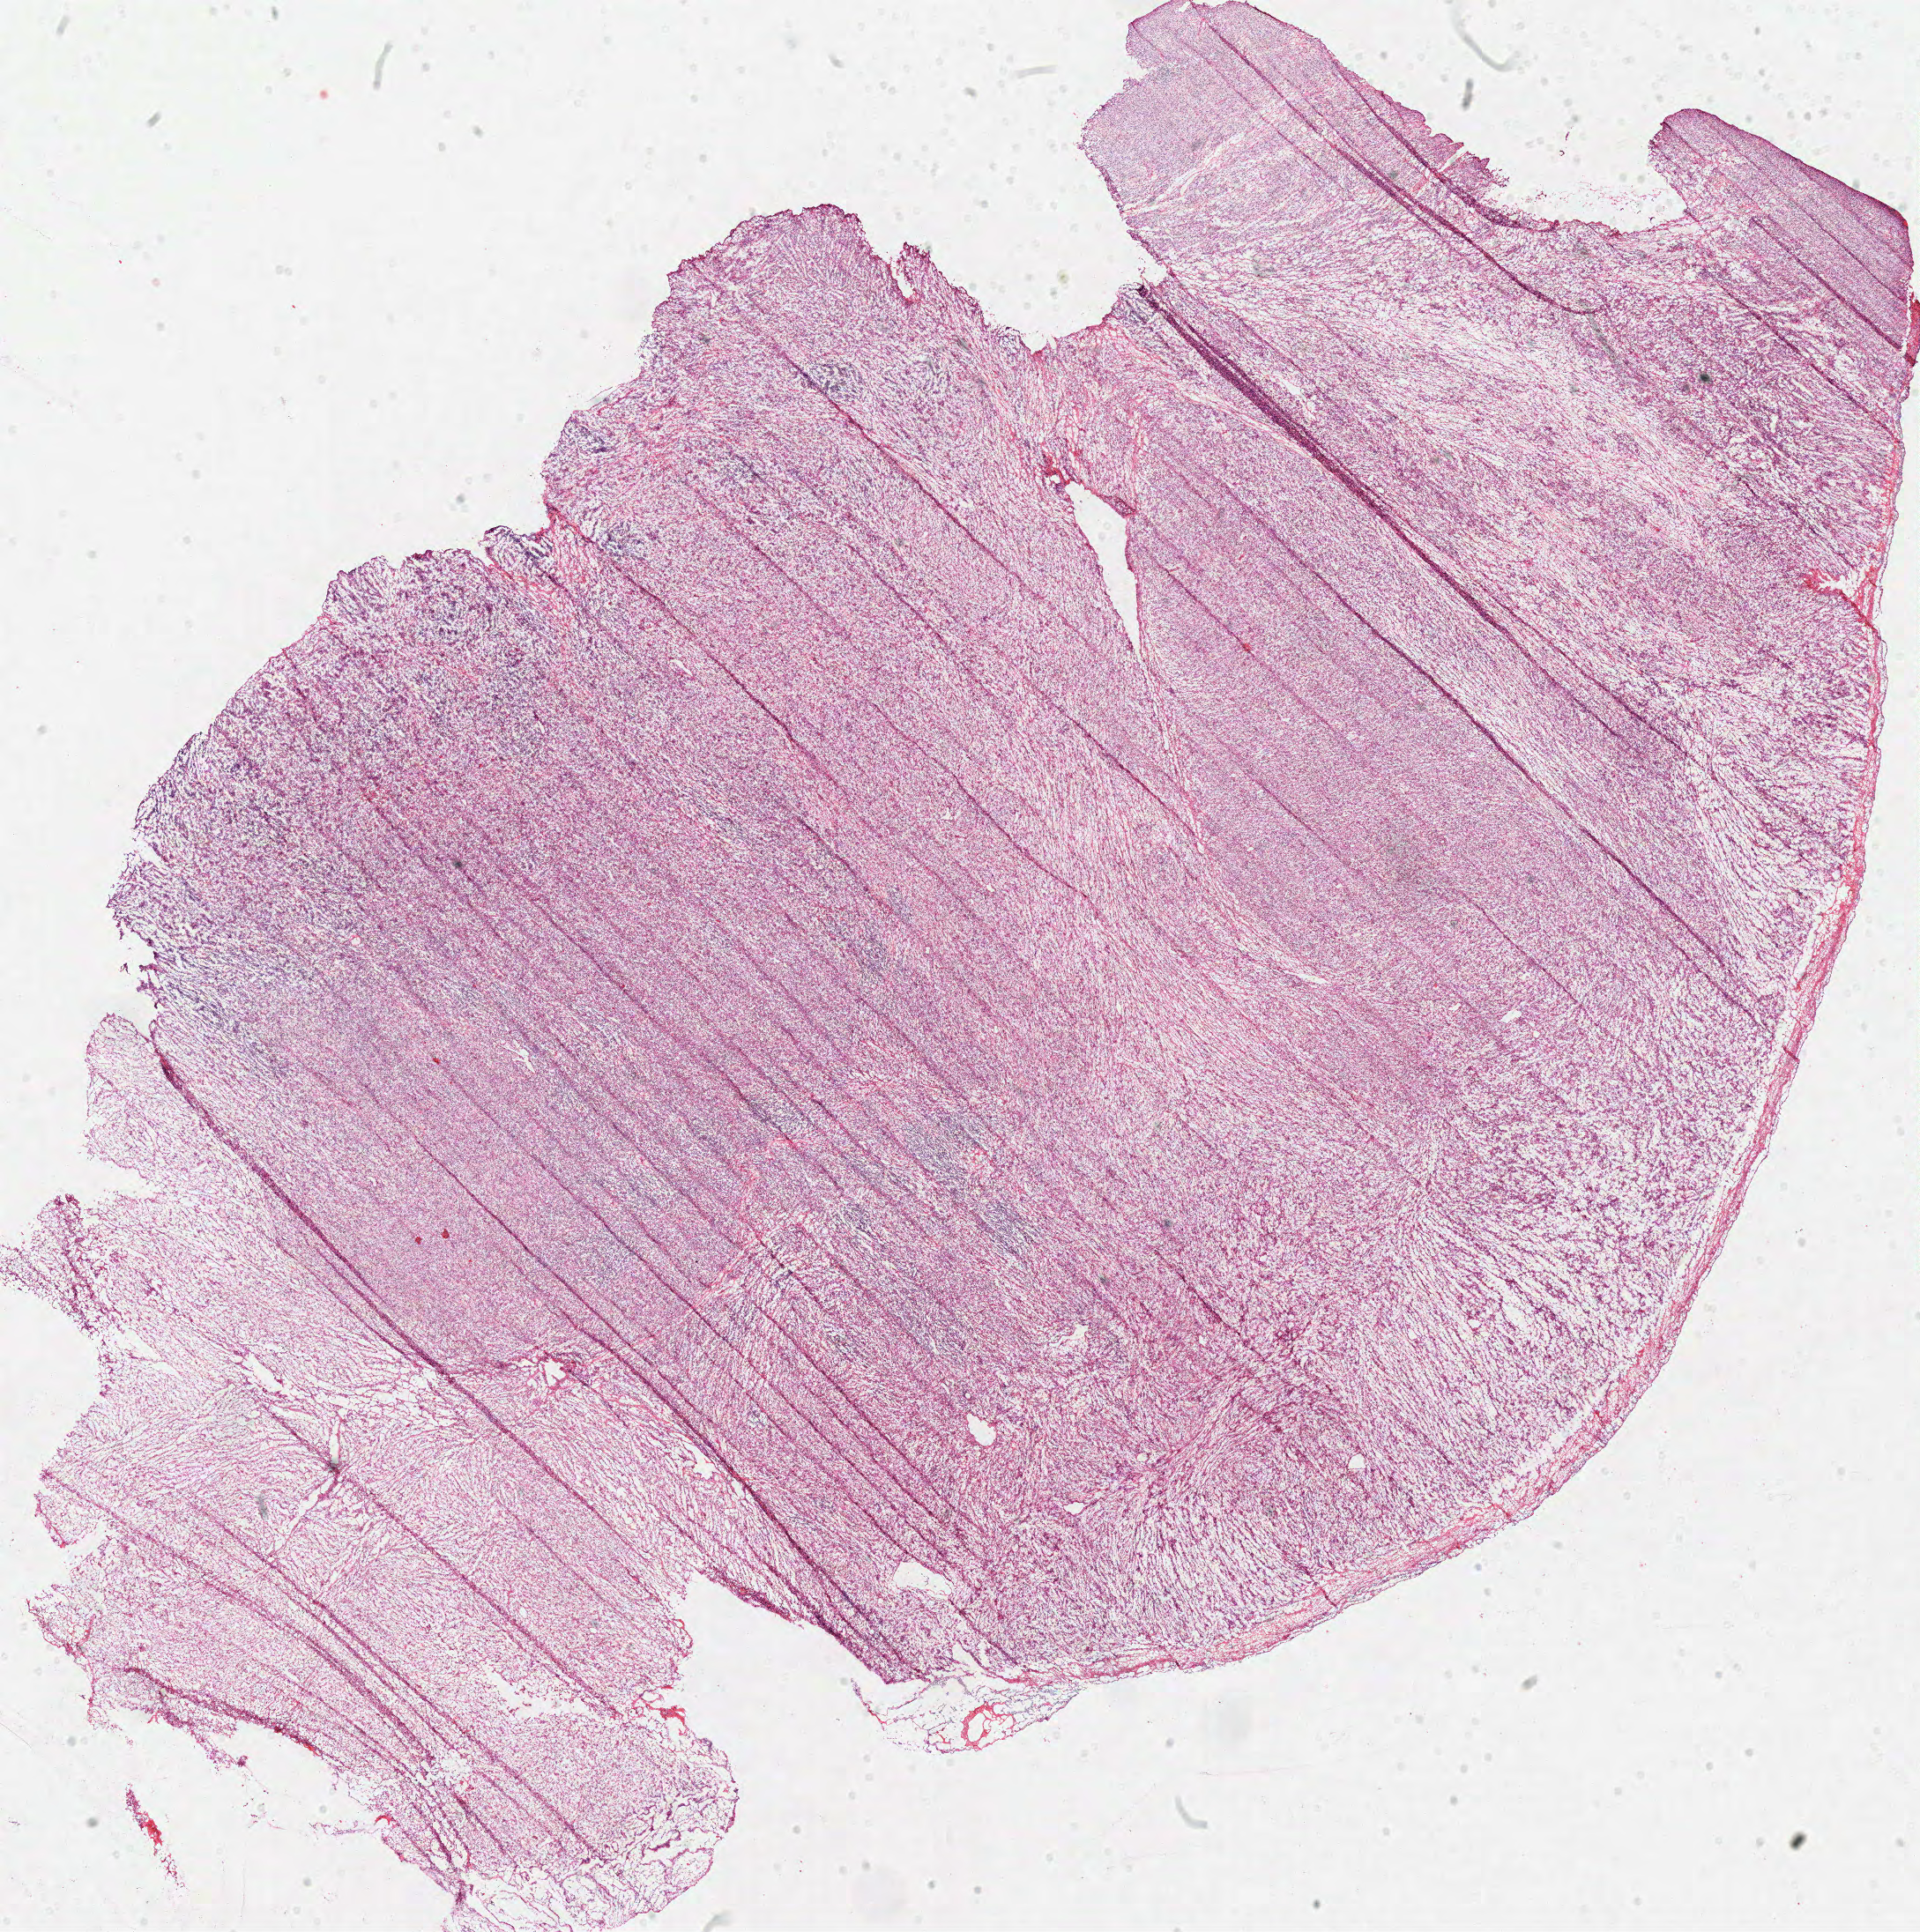
Hematoxylin and eosin (H&E) stained whole-slide image — whole scanned area (about 17.1 x 17.2 mm, from a 40x scan) shown as a low-resolution overview; frozen section from the top of the tissue portion; primary tumour sample from the stomach. Patient: female, age at initial diagnosis 57 years.
Histologic diagnosis: Adenocarcinoma, NOS (cardia, NOS).